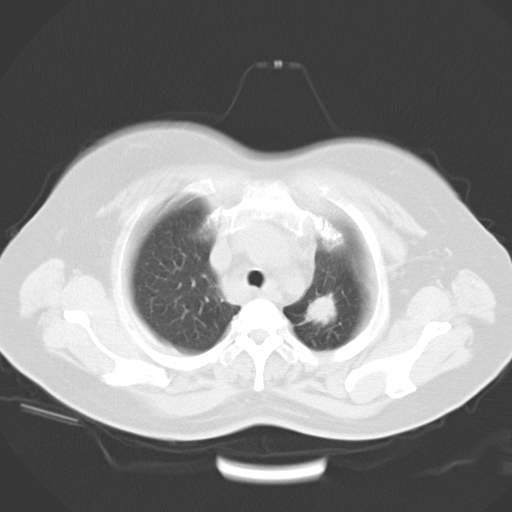
Chest CT, one axial slice; position 25 of 29 along the scan axis; reconstruction kernel B40f; 120 kVp; lung window (W 1500 / L -600 HU); 10 mm slice thickness; 512 × 512 image matrix, field of view 390 × 390 mm. Patient: female, 53 years. From the clinical record (not read from this slice): clinical TNM (as recorded): T1c N3 M0.
Outlined on this slice (rectangle marked by the reading radiologist):
- lung tumour (recorded histology: adenocarcinoma): bounding box <306,290,340,327> (left, top, right, bottom; pixels)